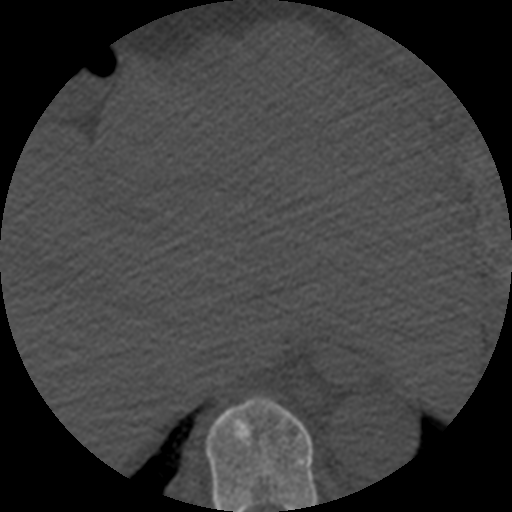
CT including the spine, one axial slice; slice 289 of 508 in the series (ordered by position); 120 kVp; bone window (W 1800 / L 400 HU); 1.25 mm slice thickness; 512 × 512 image matrix, field of view 160 × 160 mm. Patient age 57 years. From the clinical record (not read from this slice): primary cancer: prostate.
Structures marked on this image (semi-automatically segmented with operator editing):
- T9 vertebra: bounding box [x1, y1, x2, y2] px = [206, 397, 318, 512]